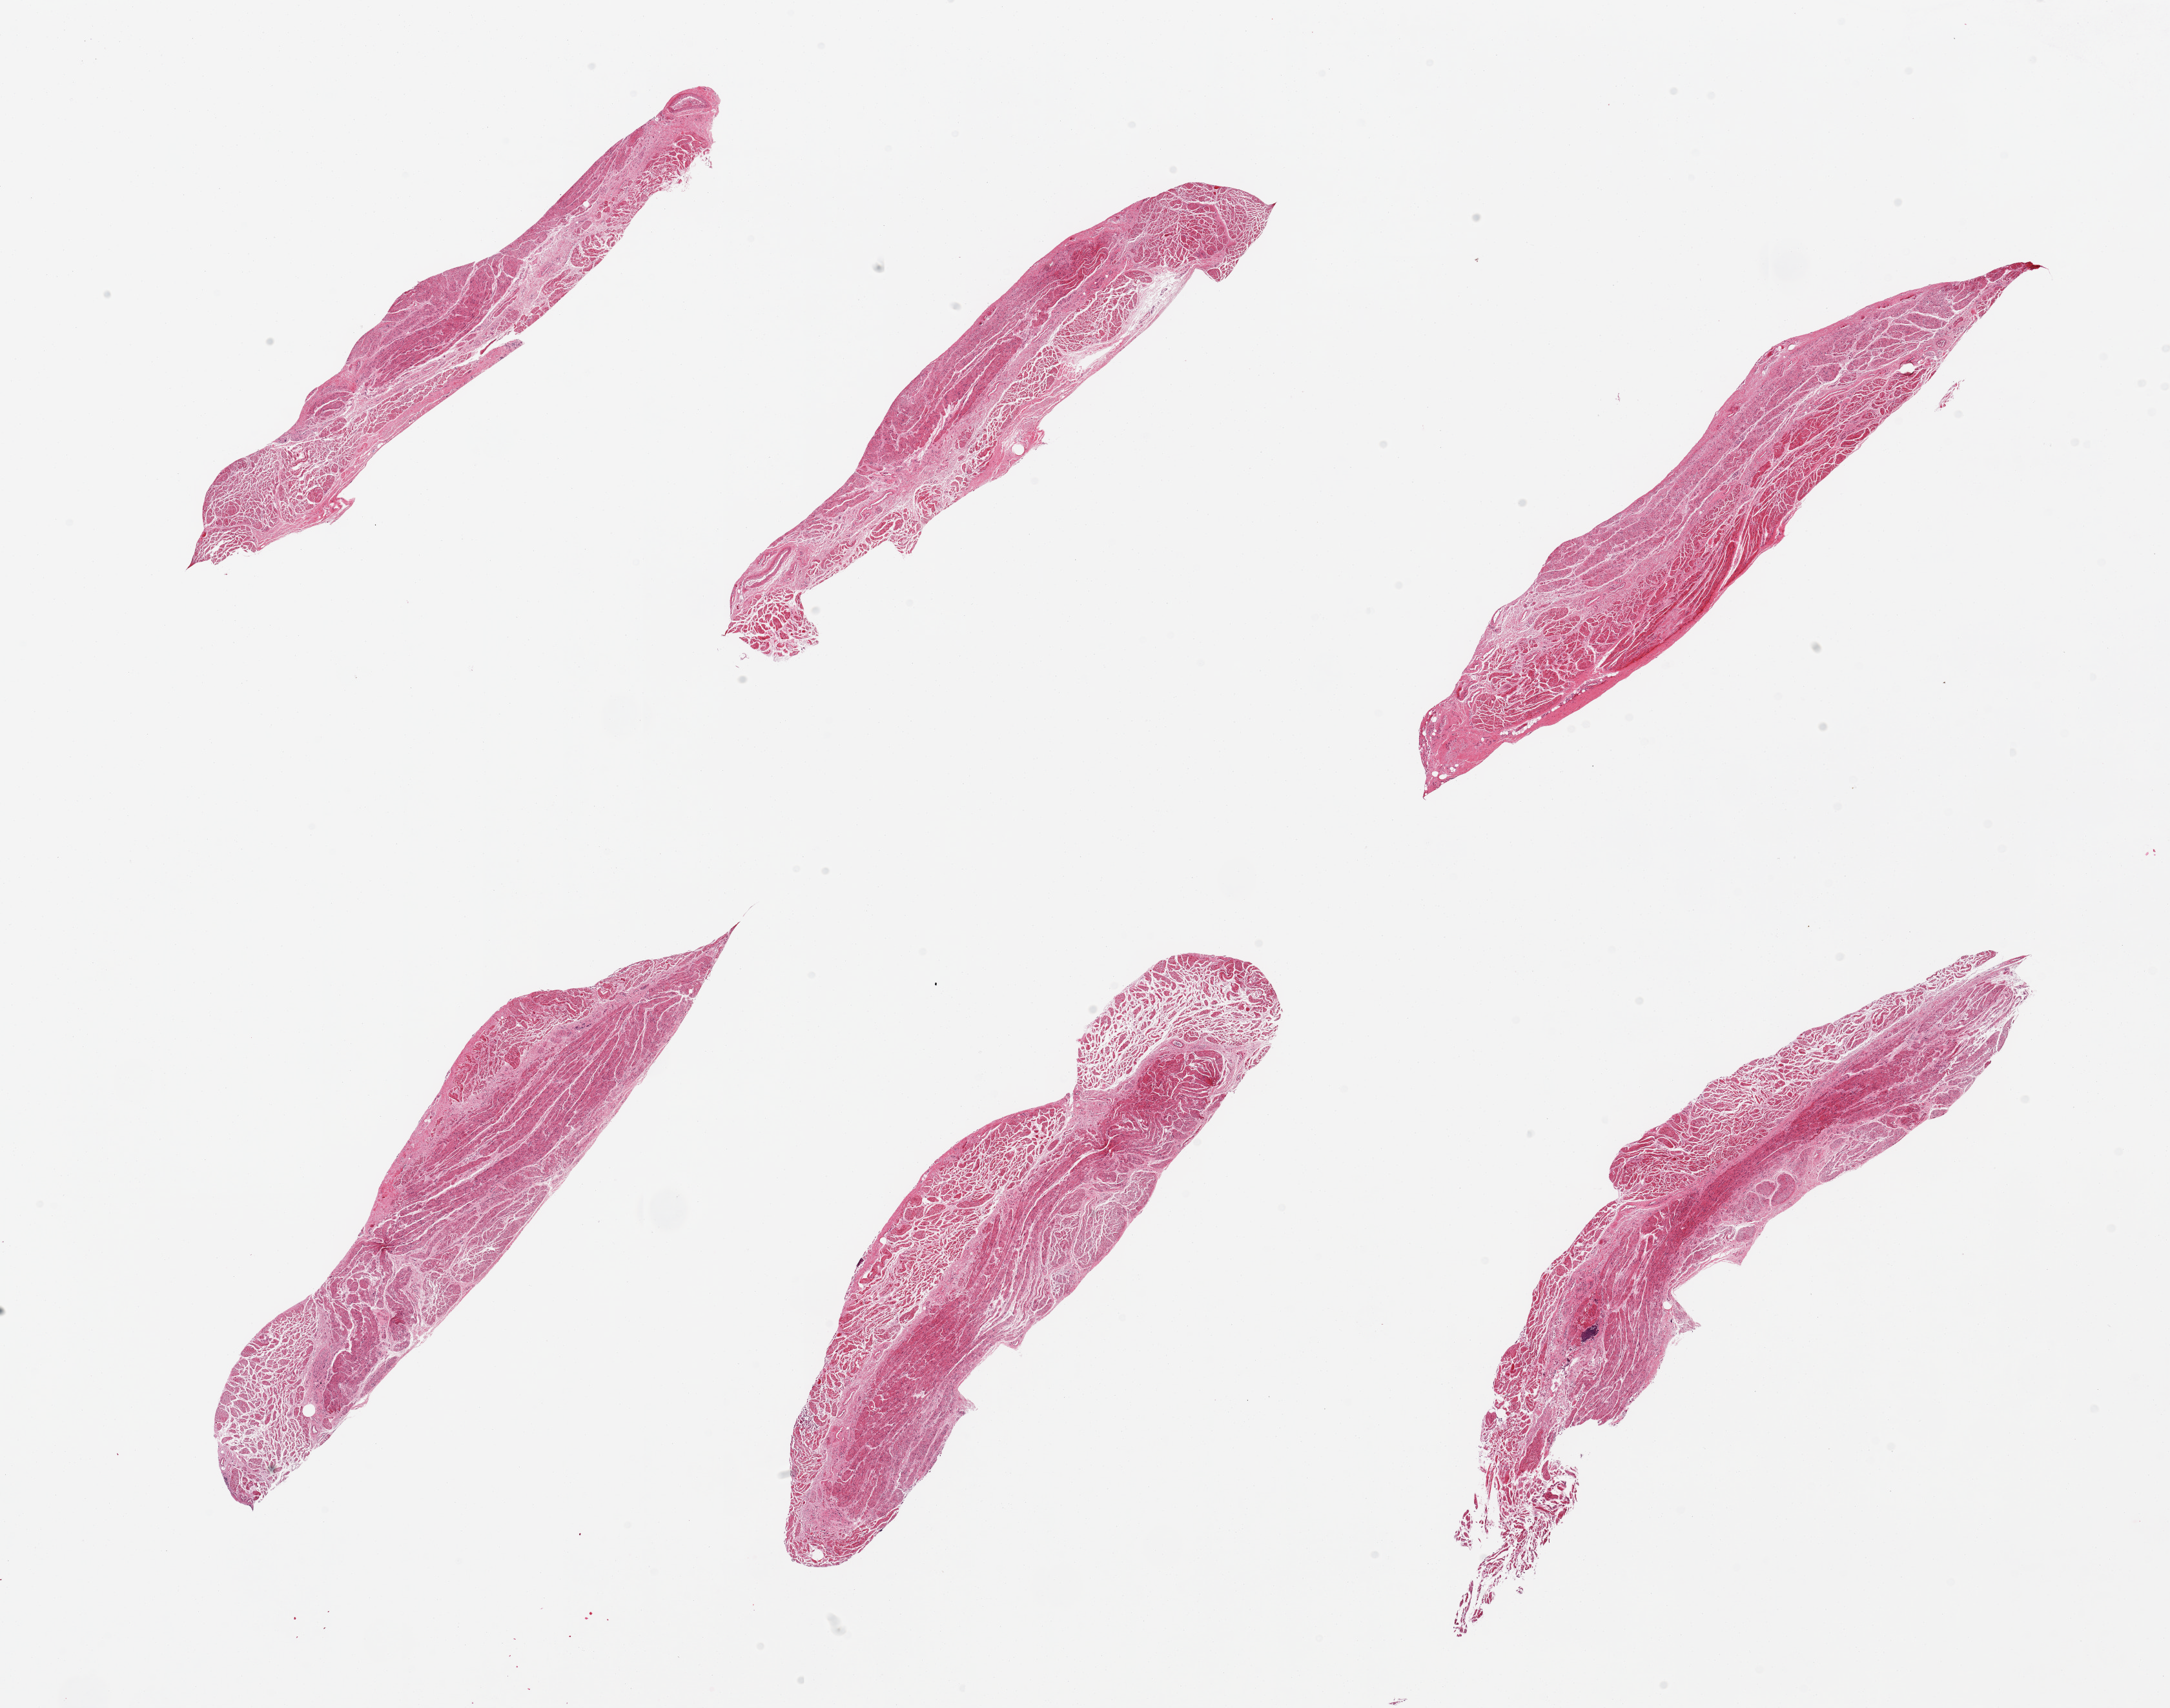
Haematoxylin and eosin whole-slide image, low-resolution overview of the scanned area, about 26.6 x 20.9 mm (from a 20x scan). PAXgene-fixed, paraffin-embedded tissue. Sampled site (target tissue): gastroesophageal junction. Donor tissue sample. Donor sex: male.
Review note (as recorded): 6 pieces, target muscularis.